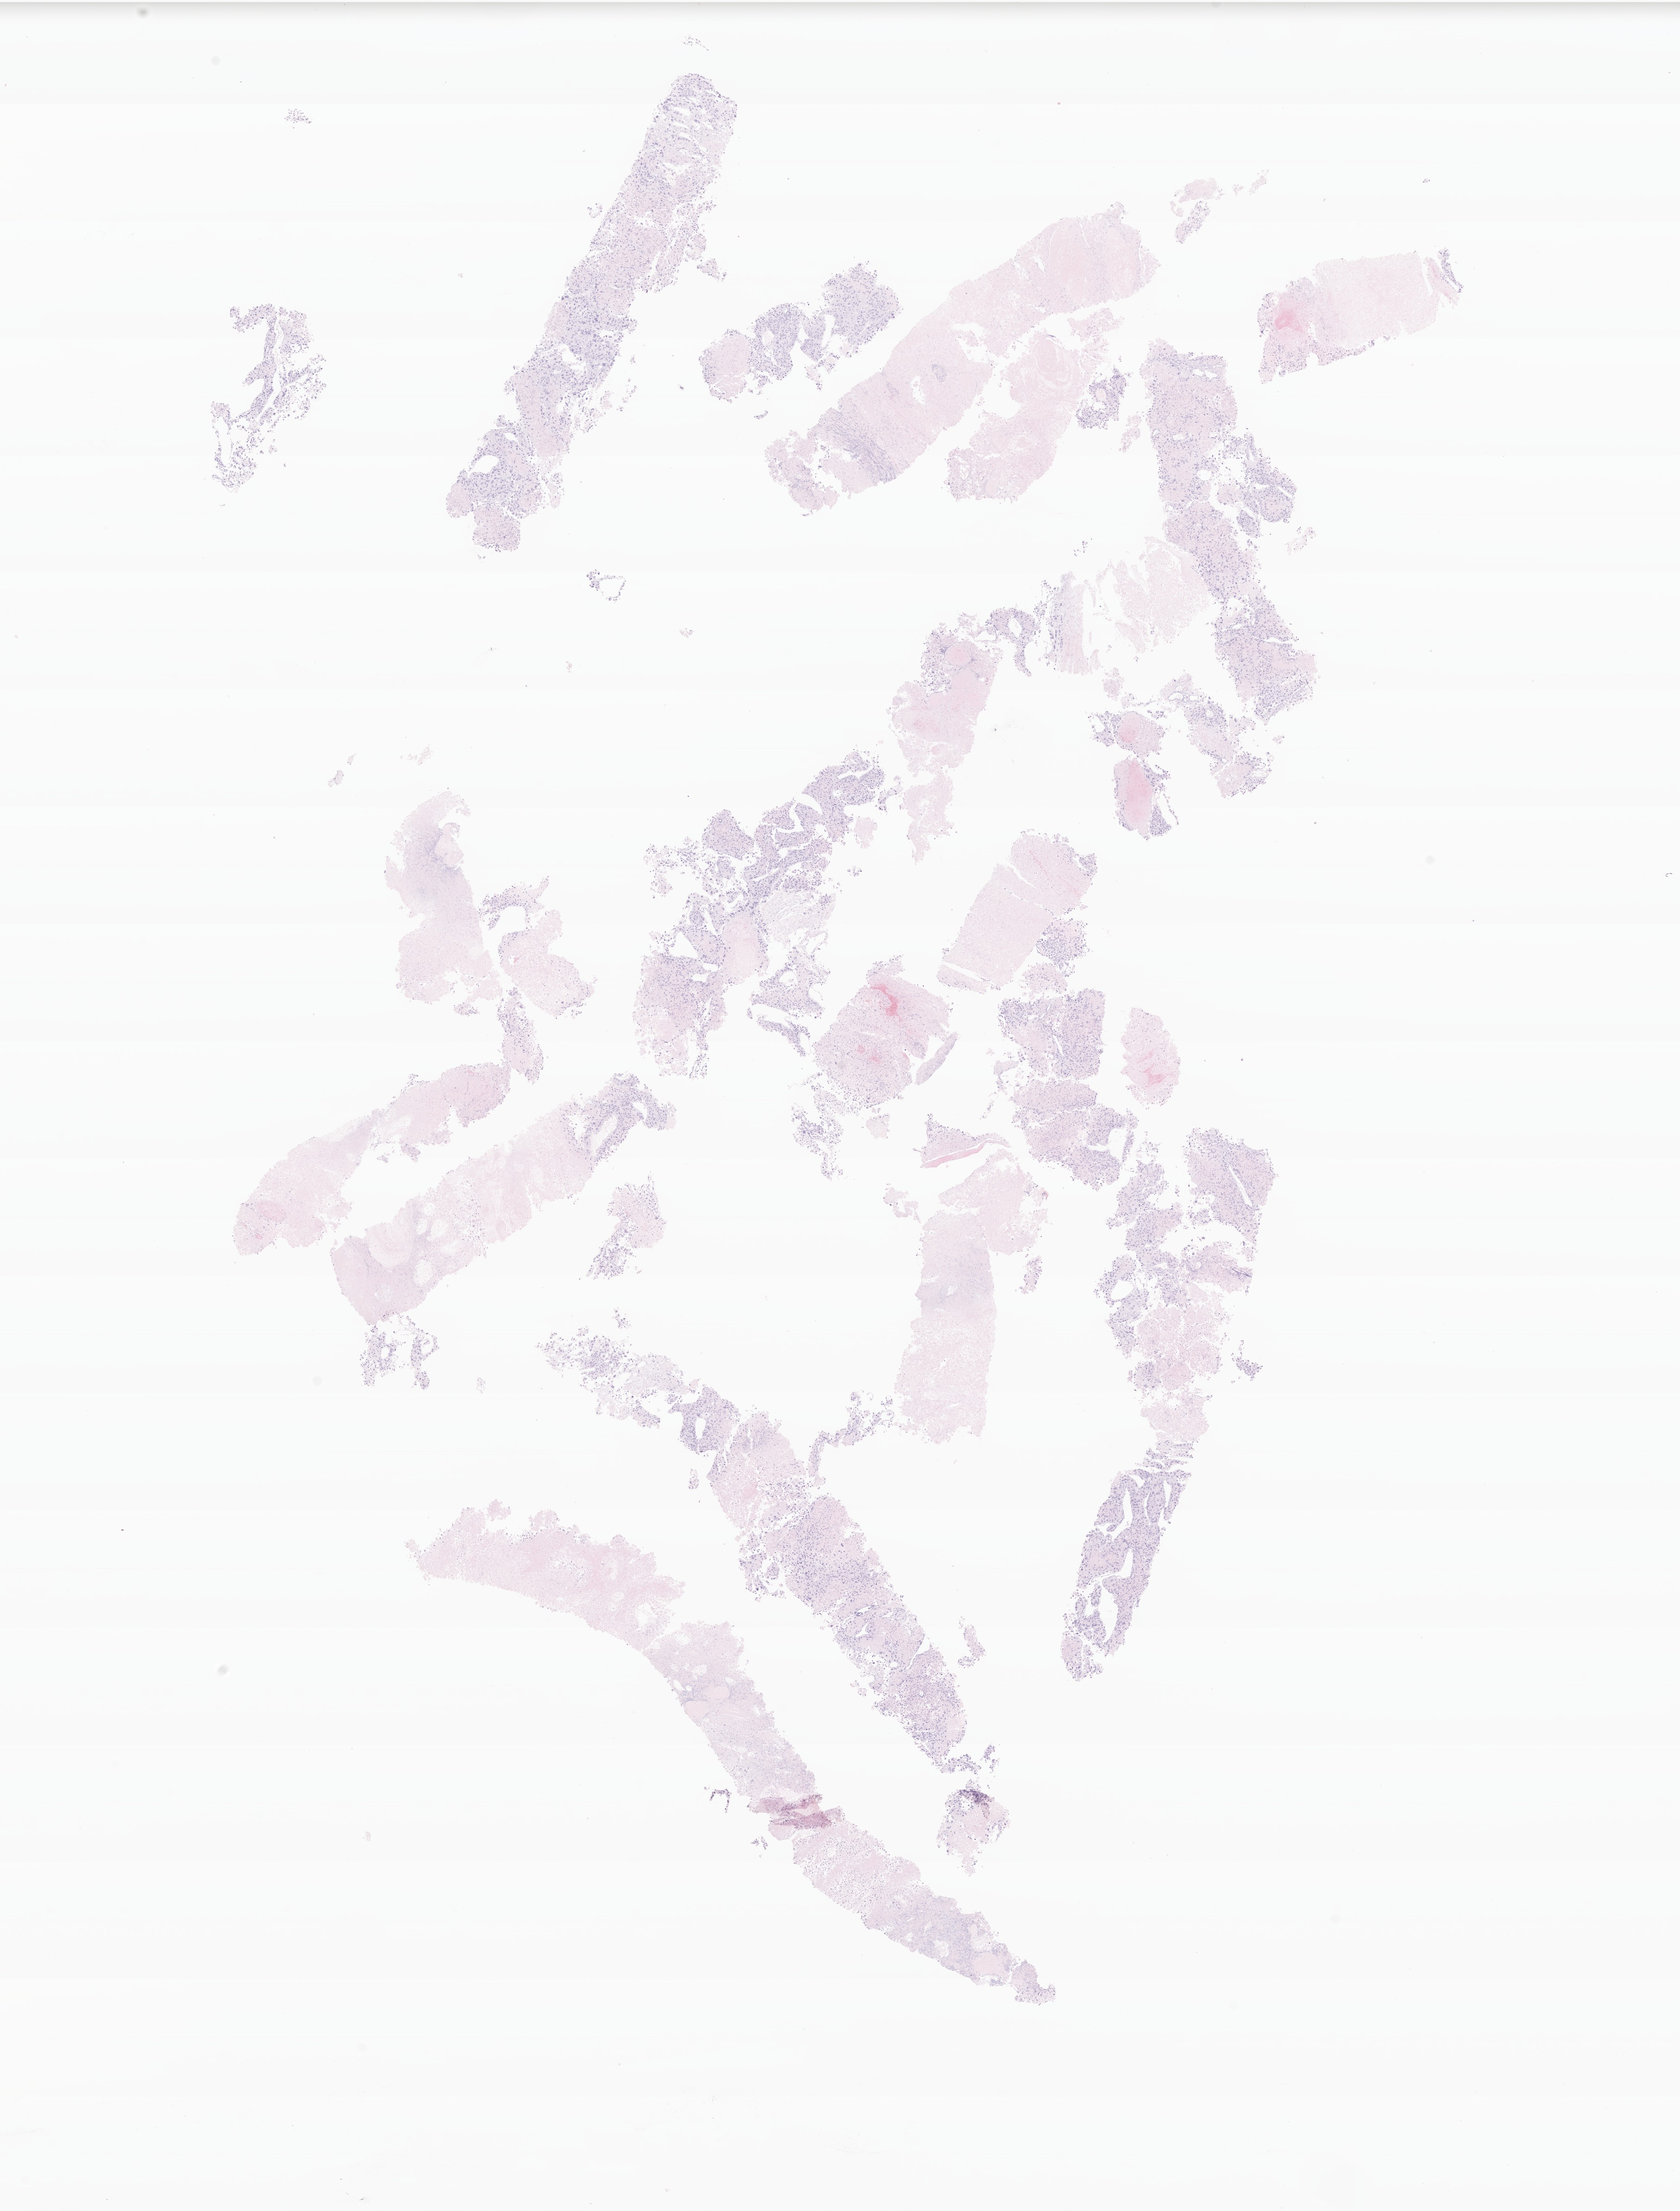
Whole-slide image, hematoxylin and eosin (H&E) stain of tumor tissue from the adrenal gland, whole scanned area (about 15.3 x 20.1 mm) shown as a low-resolution overview, formalin-fixed paraffin-embedded section. Patient female; age 196 months.
Recorded diagnosis: Adrenal cortical carcinoma.